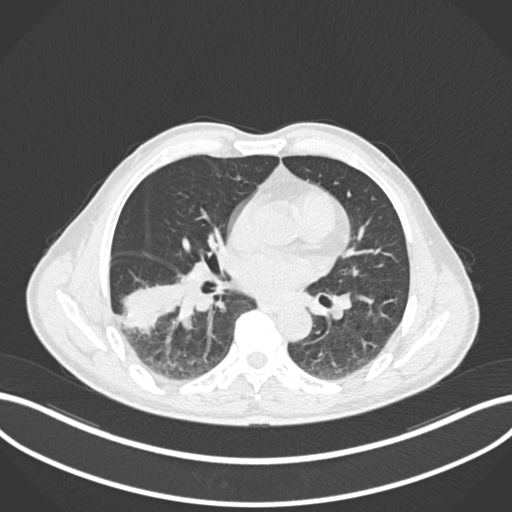
Chest CT, one axial slice. 120 kVp. Lung window (W 1500 / L -600 HU). 512 × 512 image matrix, field of view 400 × 400 mm. Male patient, age 58 years. From the clinical record (not read from this slice): clinical TNM (as recorded): T3 N0 M0; histopathological grade: G2.
Outlined on this slice (rectangle marked by the reading radiologist):
- lung tumour (recorded histology: squamous cell carcinoma): bounding box (x1, y1, x2, y2) in pixels: (115, 271, 183, 332)